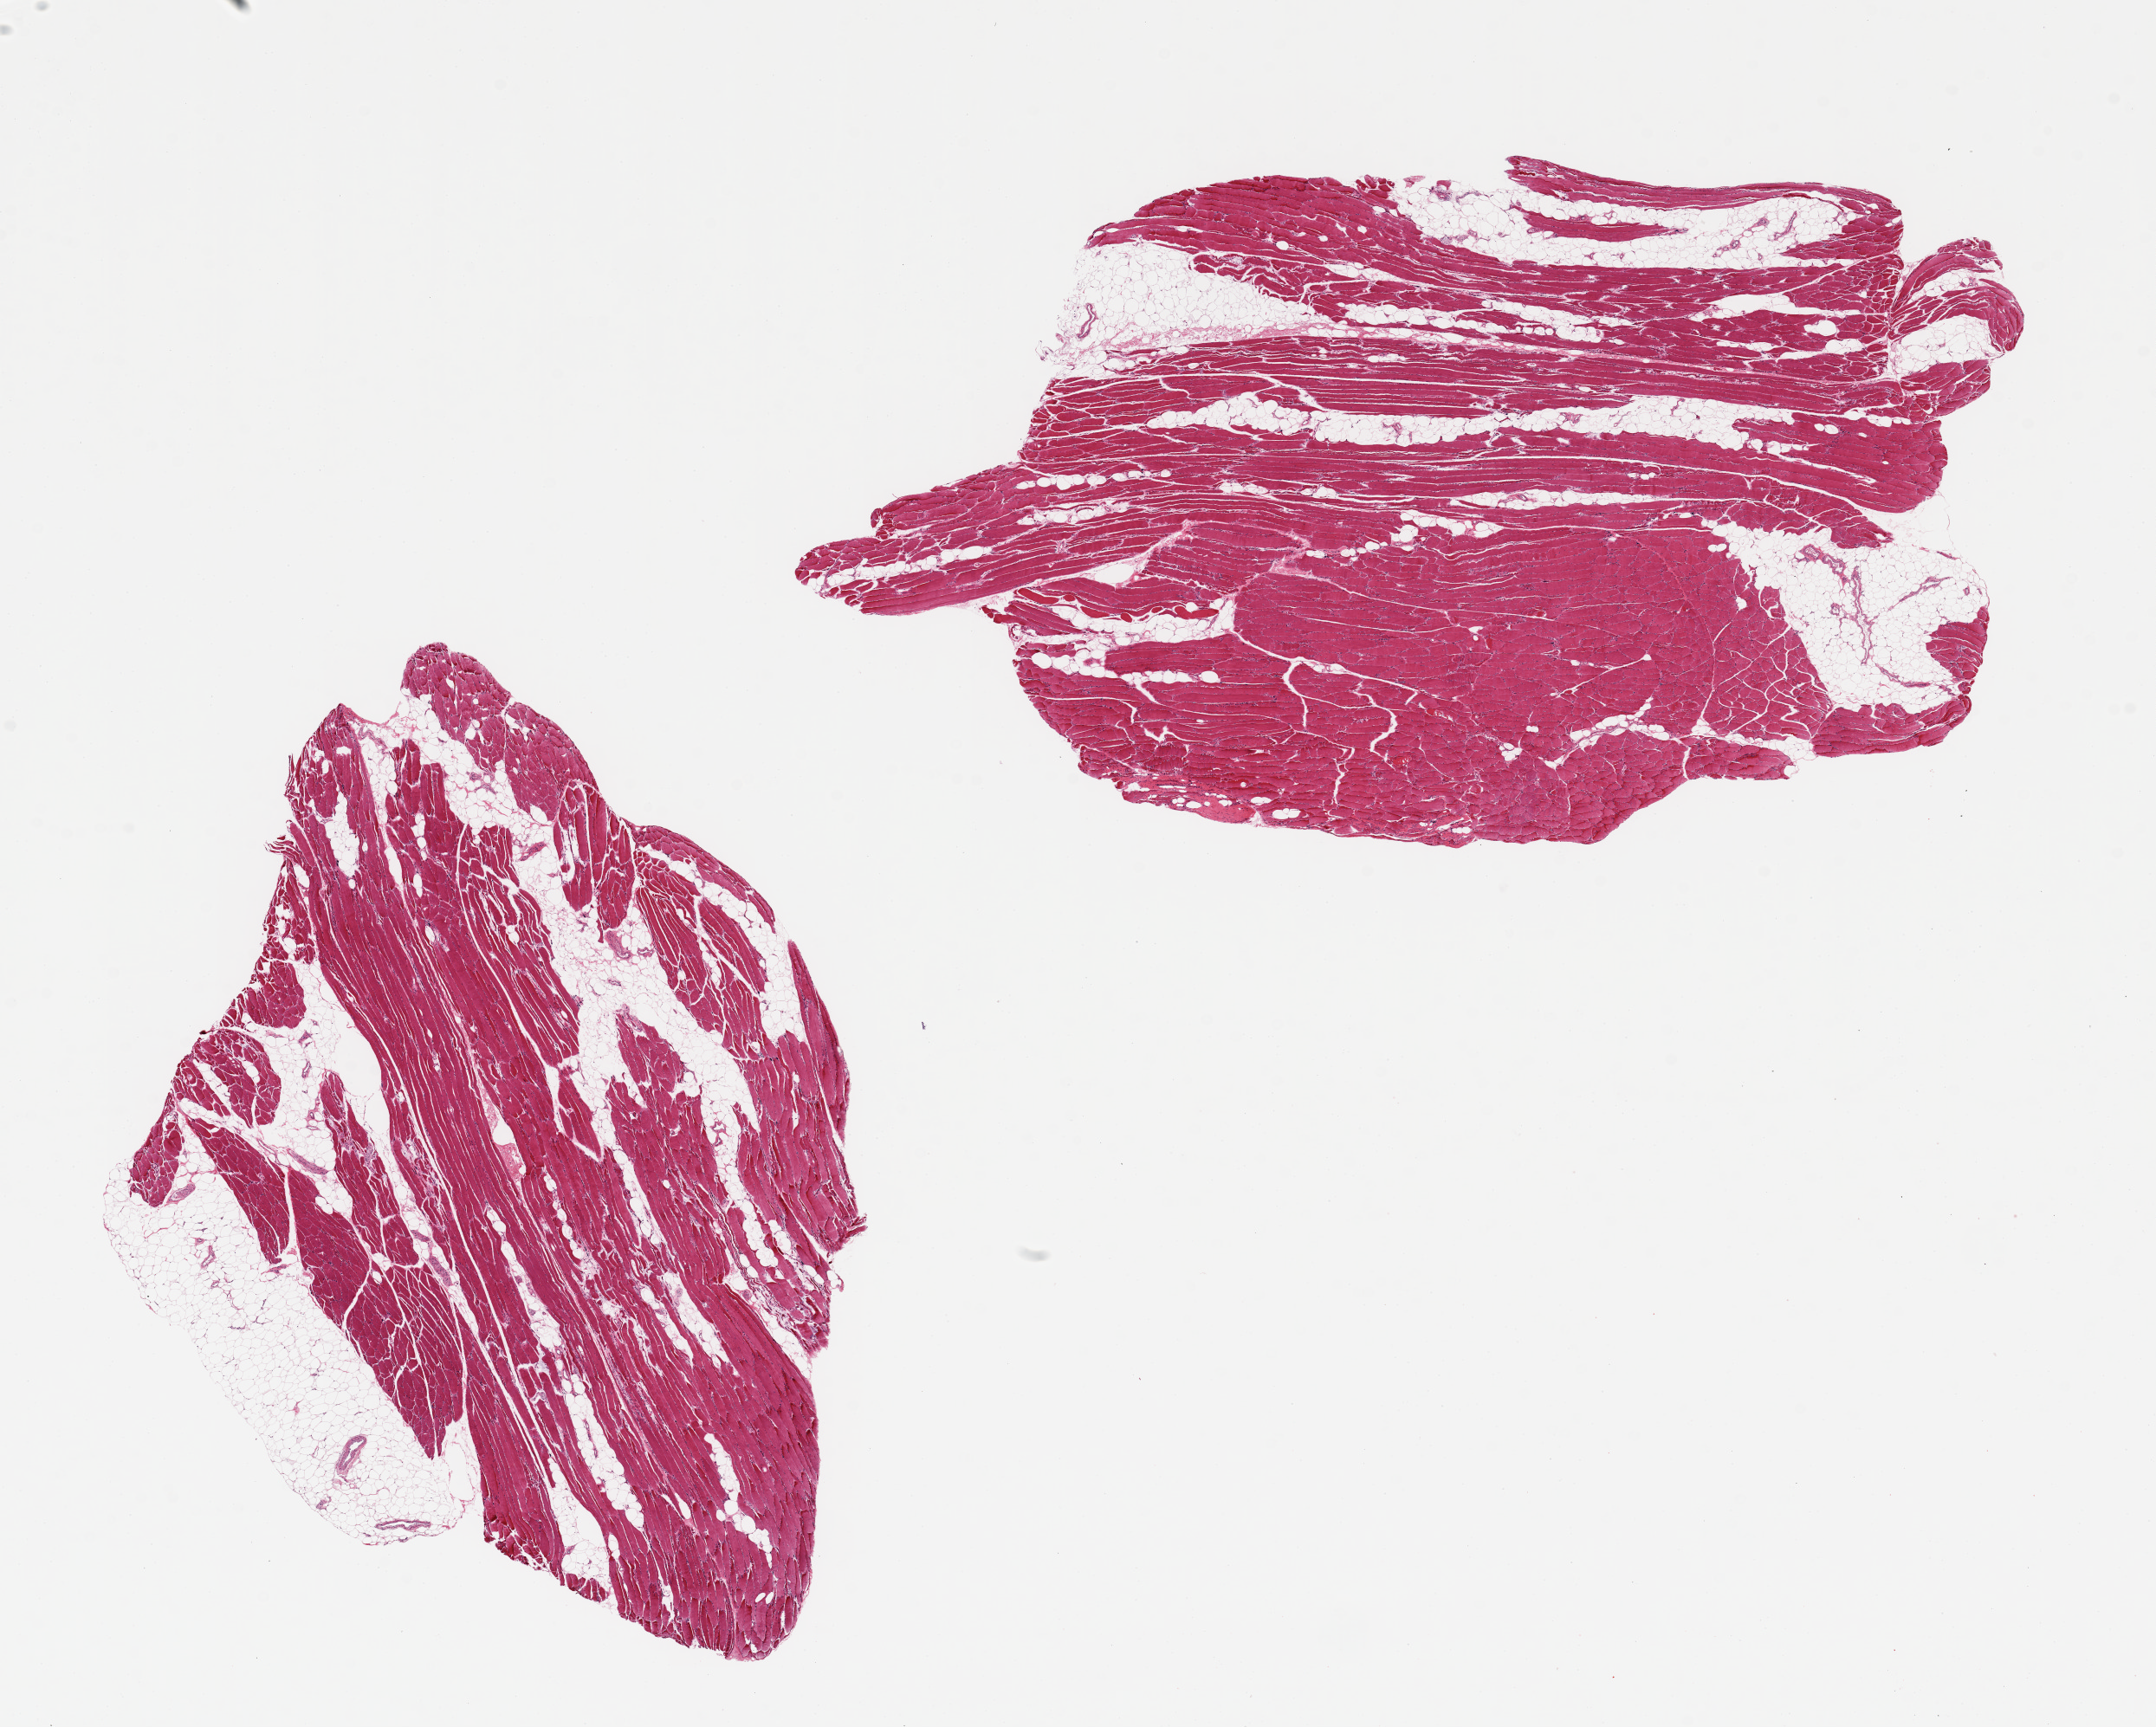
Hematoxylin and eosin (H&E) whole-slide image, shown as a low-resolution overview of the whole scanned area (about 19.7 x 15.8 mm, acquisition: 20x scan); PAXgene-fixed paraffin-embedded (PFPE) section; sampled site (target tissue): skeletal muscle; tissue donor sample. Donor sex: female.
* pathologist's review note for this sample: 2 pieces, 10x7 & 11x6mm; 10-20% interstital fat